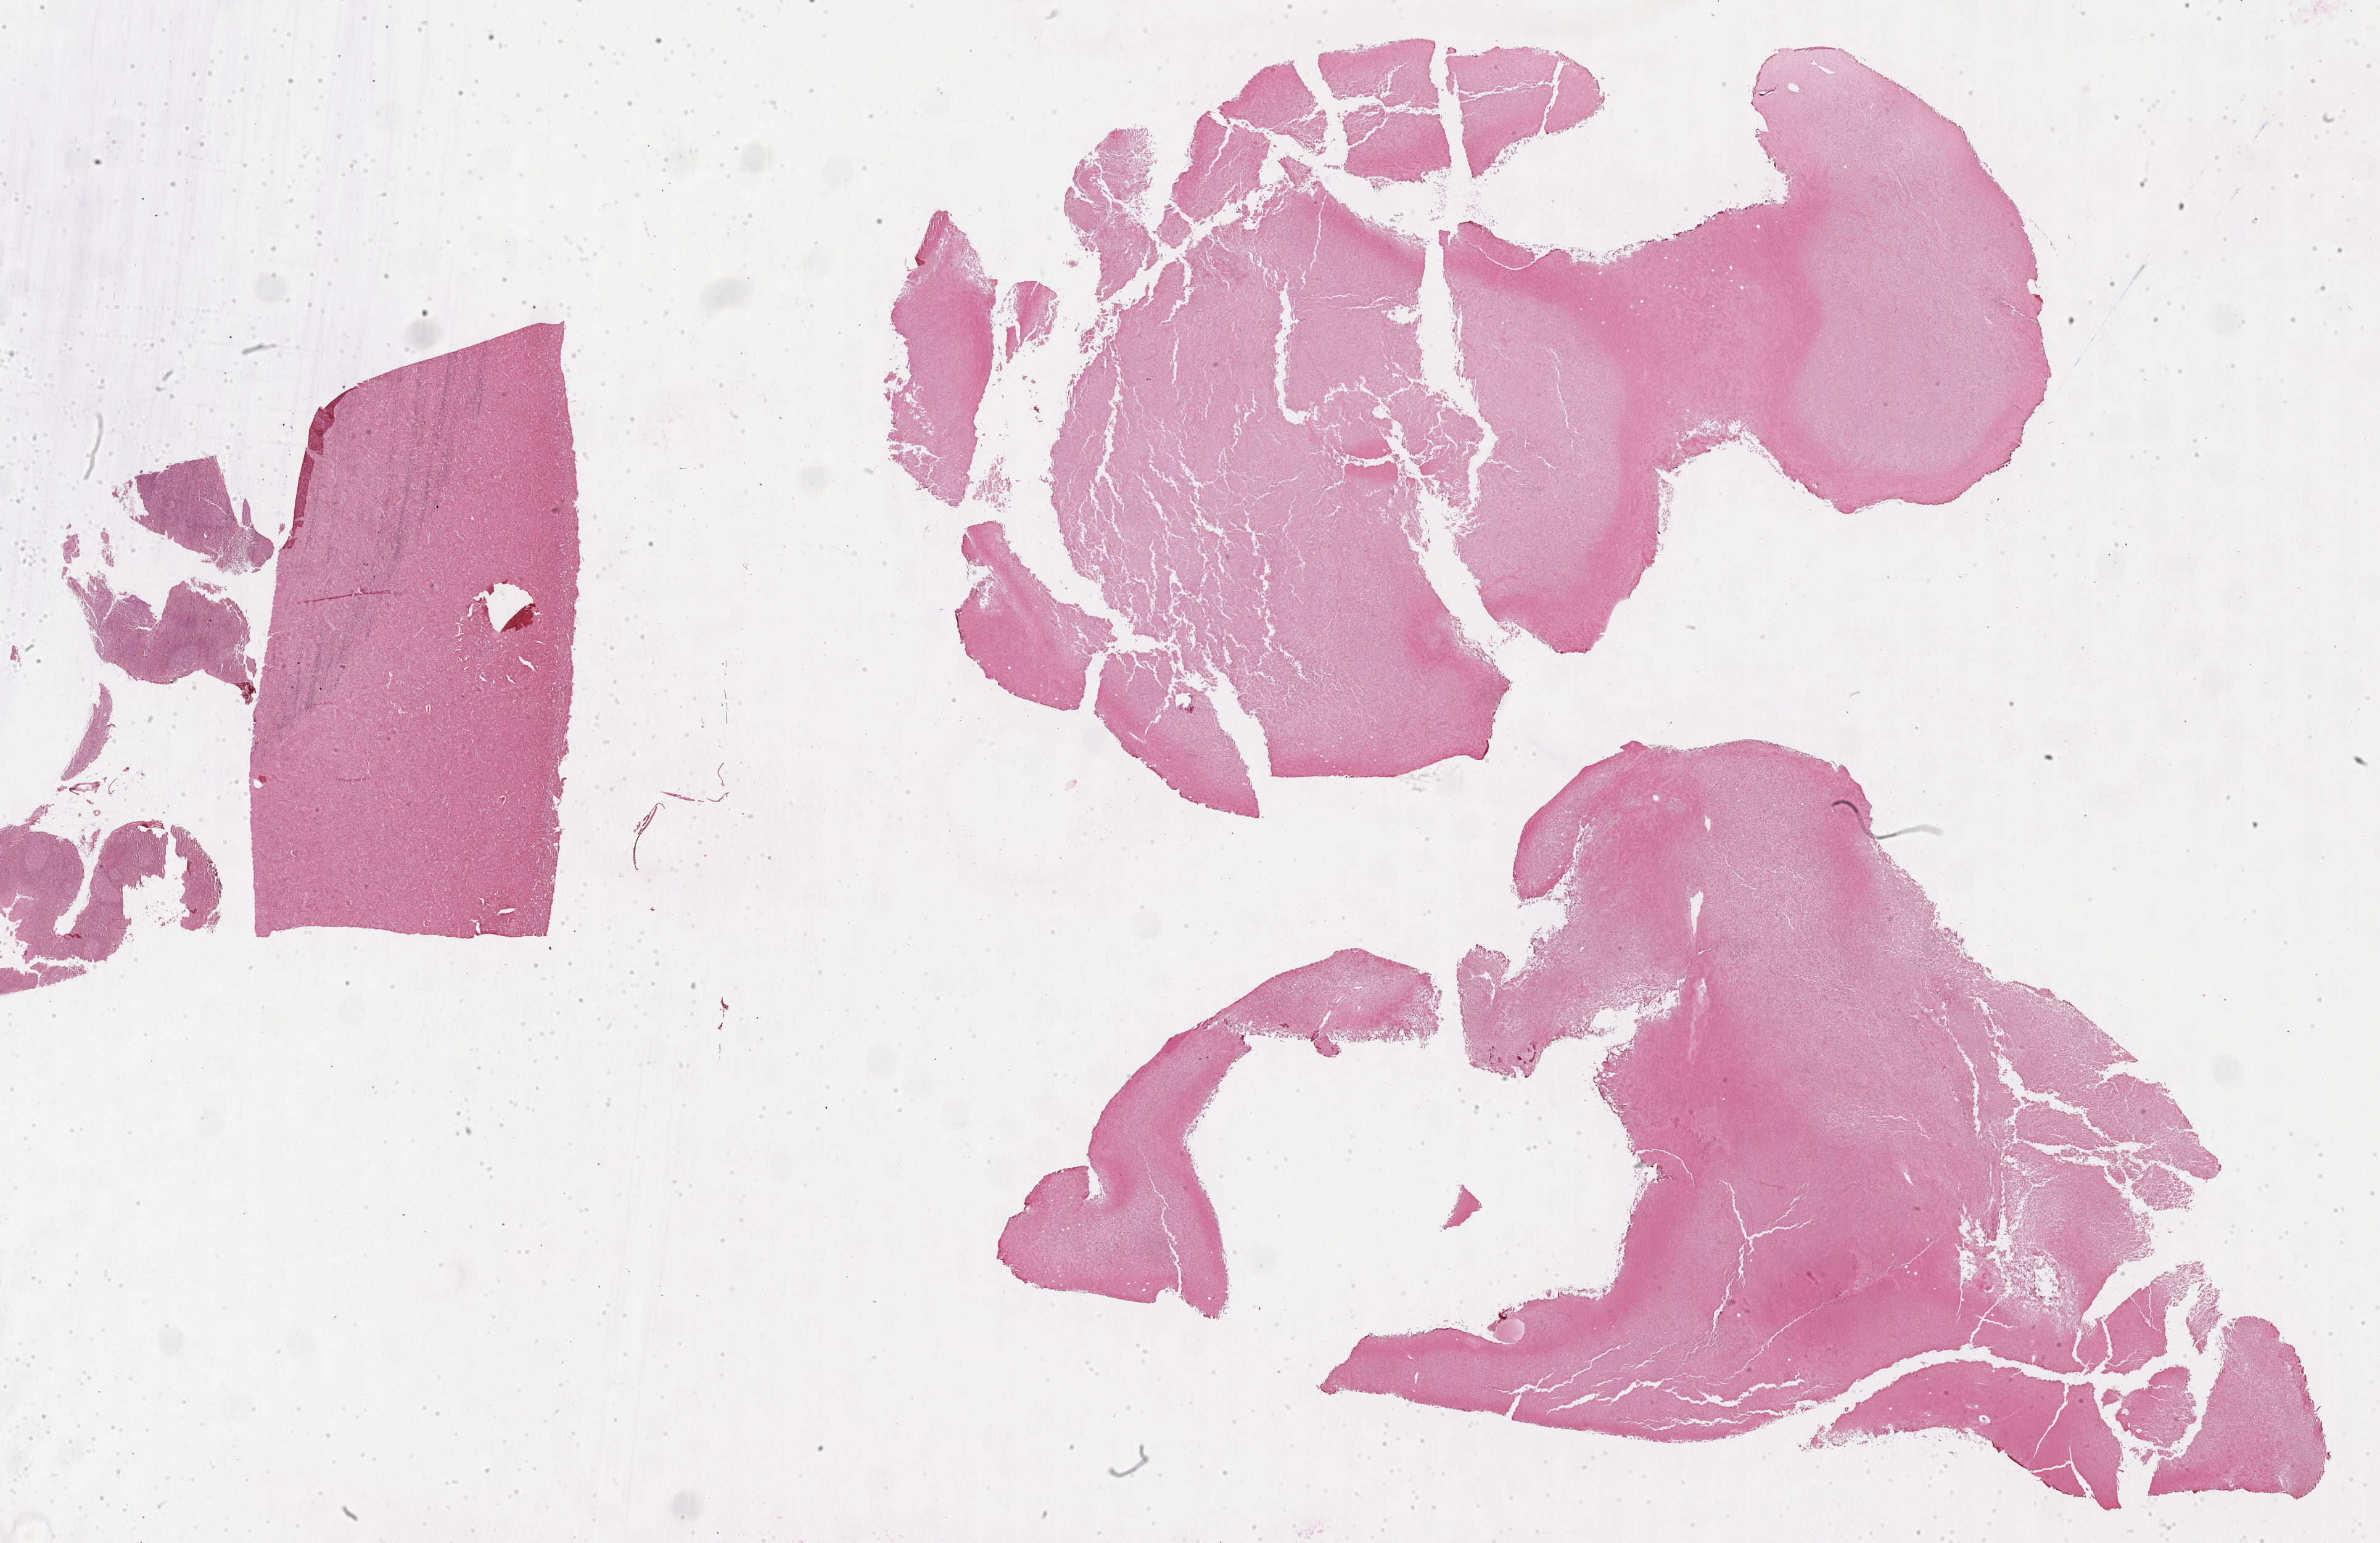
Whole-slide image, Epstein–Barr virus-encoded RNA (EBER) in-situ hybridisation, whole scanned area (about 31.2 x 20.2 mm) shown as a low-resolution overview. Specimen: tumor tissue. Anatomic site: liver. Male patient, aged 45.
Histologic diagnosis: Diffuse large B-cell lymphoma, NOS.